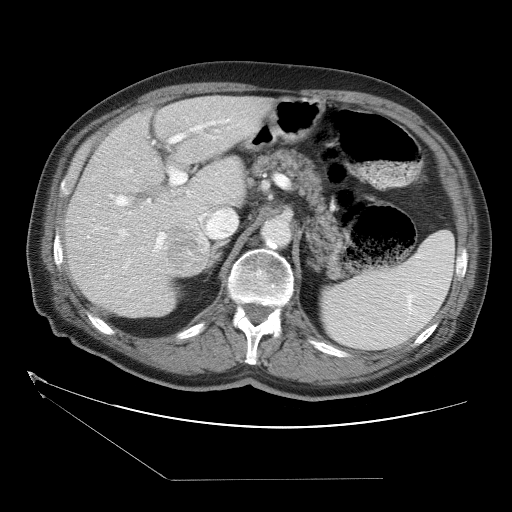
Contrast-enhanced abdominal CT (liver protocol), one axial slice; reconstruction kernel STANDARD; 120 kVp; one of 2 acquisitions stored at this slice position; soft-tissue window (W 400 / L 40 HU); 5 mm slice thickness; 512 × 512 image matrix. From the clinical record (not read from this slice): diagnosis: hepatocellular carcinoma (patient treated with transarterial chemoembolisation; whether this scan precedes or follows treatment is not stated here); TNM stage (as recorded): Stage-II; Child-Pugh class: A; tumour differentiation: moderately differentiated; tumour nodularity: multinodular.
Annotated regions visible in this slice (semi-automatic segmentation, software-assisted and operator-edited):
- liver parenchyma outside the tumour (the mass and vessels are separate outlines, so this box may not span the whole liver): bounding box <64,96,272,318> (left, top, right, bottom; pixels)
- mass: <163,223,210,277>
- liver vessels: <87,120,231,298>